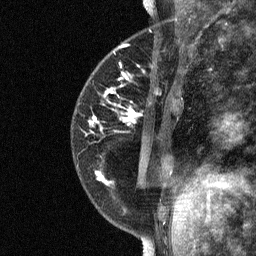
Breast MRI (dynamic contrast-enhanced), one sagittal slice; slice 21 of 64 in the series (ordered by position); dynamic contrast-enhanced study with each time point stored as its own series, time point 2 of 3 at this slice position (early post-contrast, ordered by acquisition time); 1.5 T; TE 4.8 ms, TR 27 ms; 2 mm slice thickness; 256 × 256 image matrix, field of view 180 × 180 mm. Female patient, age 34 years. From the clinical record (not read from this slice): setting: breast cancer imaged before/during neoadjuvant chemotherapy; receptor status: HR-positive, HER2-negative.
Annotated regions visible in this slice (semi-automatically segmented with operator editing):
- analysis volume of interest (the breast-tissue region the enhancement analysis was run in; not a lesion): bounding box [x1, y1, x2, y2] px = [78, 44, 181, 191]
- tumour enhancement mask (voxels above the 90 % enhancement threshold inside the analysis volume of interest): [93, 73, 141, 184]